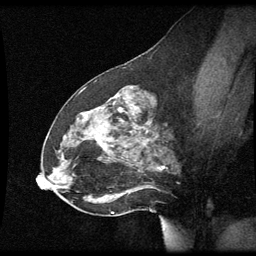
Breast MRI (dynamic contrast-enhanced), one sagittal slice; position 31 of 60 along the scan axis; dynamic contrast-enhanced series, image 2 of 3 at this slice position (ordered by acquisition); 1.5 T; TE 4.2 ms, TR 8.9 ms; 2 mm slice thickness; 256 × 256 image matrix, field of view 200 × 200 mm. Patient: female, 49 years. Case-level facts recorded for this patient, not image findings: setting: breast cancer imaged before/during neoadjuvant chemotherapy; receptor status: HR-positive, HER2-negative.
Outlined on this slice (semi-automatic segmentation, software-assisted and operator-edited):
- analysis volume of interest (the breast-tissue region the enhancement analysis was run in; not a lesion): bounding box [x1, y1, x2, y2] px = [46, 92, 177, 205]
- tumour enhancement mask (voxels above the 70 % enhancement threshold inside the analysis volume of interest): [120, 108, 122, 111]